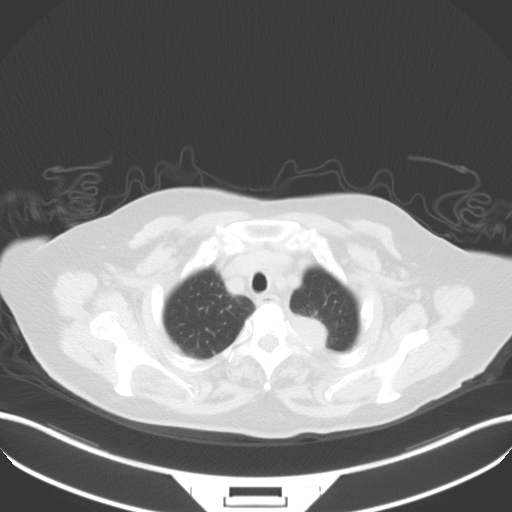
Chest CT, one axial slice; position 36 of 42 along the scan axis; lung window (W 1500 / L -600 HU); 6 mm slice thickness; 512 × 512 image matrix, field of view 400 × 400 mm. Patient: female, 81 years. From the clinical record (not read from this slice): clinical TNM (as recorded): T2a N0 M0.
Structures marked on this image (rectangle marked by the reading radiologist):
- lung tumour (recorded histology: adenocarcinoma): bounding box [x1, y1, x2, y2] px = [287, 306, 332, 359]